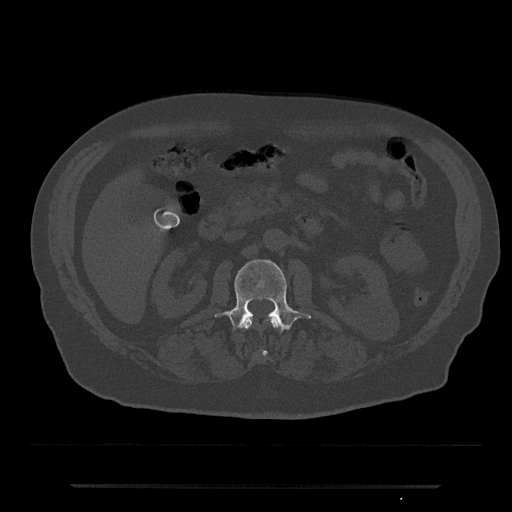
CT including the spine, one axial slice; slice 486 of 797 in the series (ordered by position); bone window (W 1800 / L 400 HU); 0.5 mm slice thickness; 512 × 512 image matrix. Patient: male, 80 years. From the clinical record (not read from this slice): primary cancer: prostate.
Annotated regions visible in this slice (semi-automatically segmented with operator editing):
- L1 vertebra: box from (x=243, y=317) to (x=281, y=355) px
- L2 vertebra: (x=214, y=259)–(x=311, y=331)